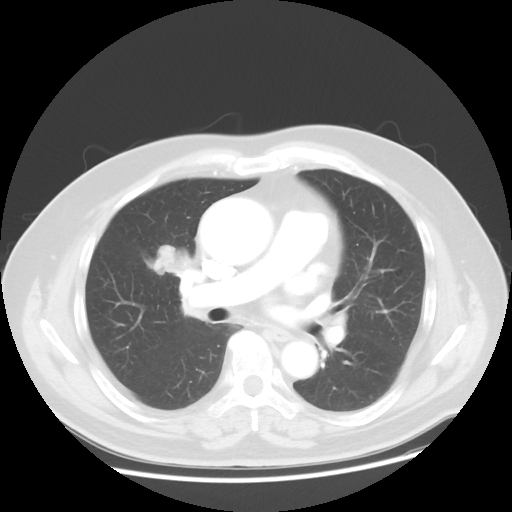
Chest CT, one axial slice. Position 25 of 48 along the scan axis. Reconstruction kernel STANDARD. 120 kVp. Lung window (W 1500 / L -600 HU). 5 mm slice thickness. 512 × 512 image matrix, field of view 392 × 392 mm. Patient: male, 60 years. From the clinical record (not read from this slice): clinical TNM (as recorded): T2 N3 M0.
Structures marked on this image (rectangle marked by the reading radiologist):
- lung tumour (recorded histology: adenocarcinoma): bounding box (x1, y1, x2, y2) in pixels: (148, 240, 194, 286)